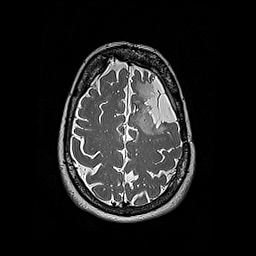
Brain MRI from a brain-tumour surgery series, one axial slice; slice 138 of 192 in the series (ordered by position); 256 × 256 image matrix. Case-level facts recorded for this patient, not image findings: histopathology: Oligodendroglioma; WHO grade: 2; IDH mutation: yes.
Outlined on this slice (manually delineated by an expert):
- tumour: bounding box (x1, y1, x2, y2) in pixels: (144, 114, 157, 134)